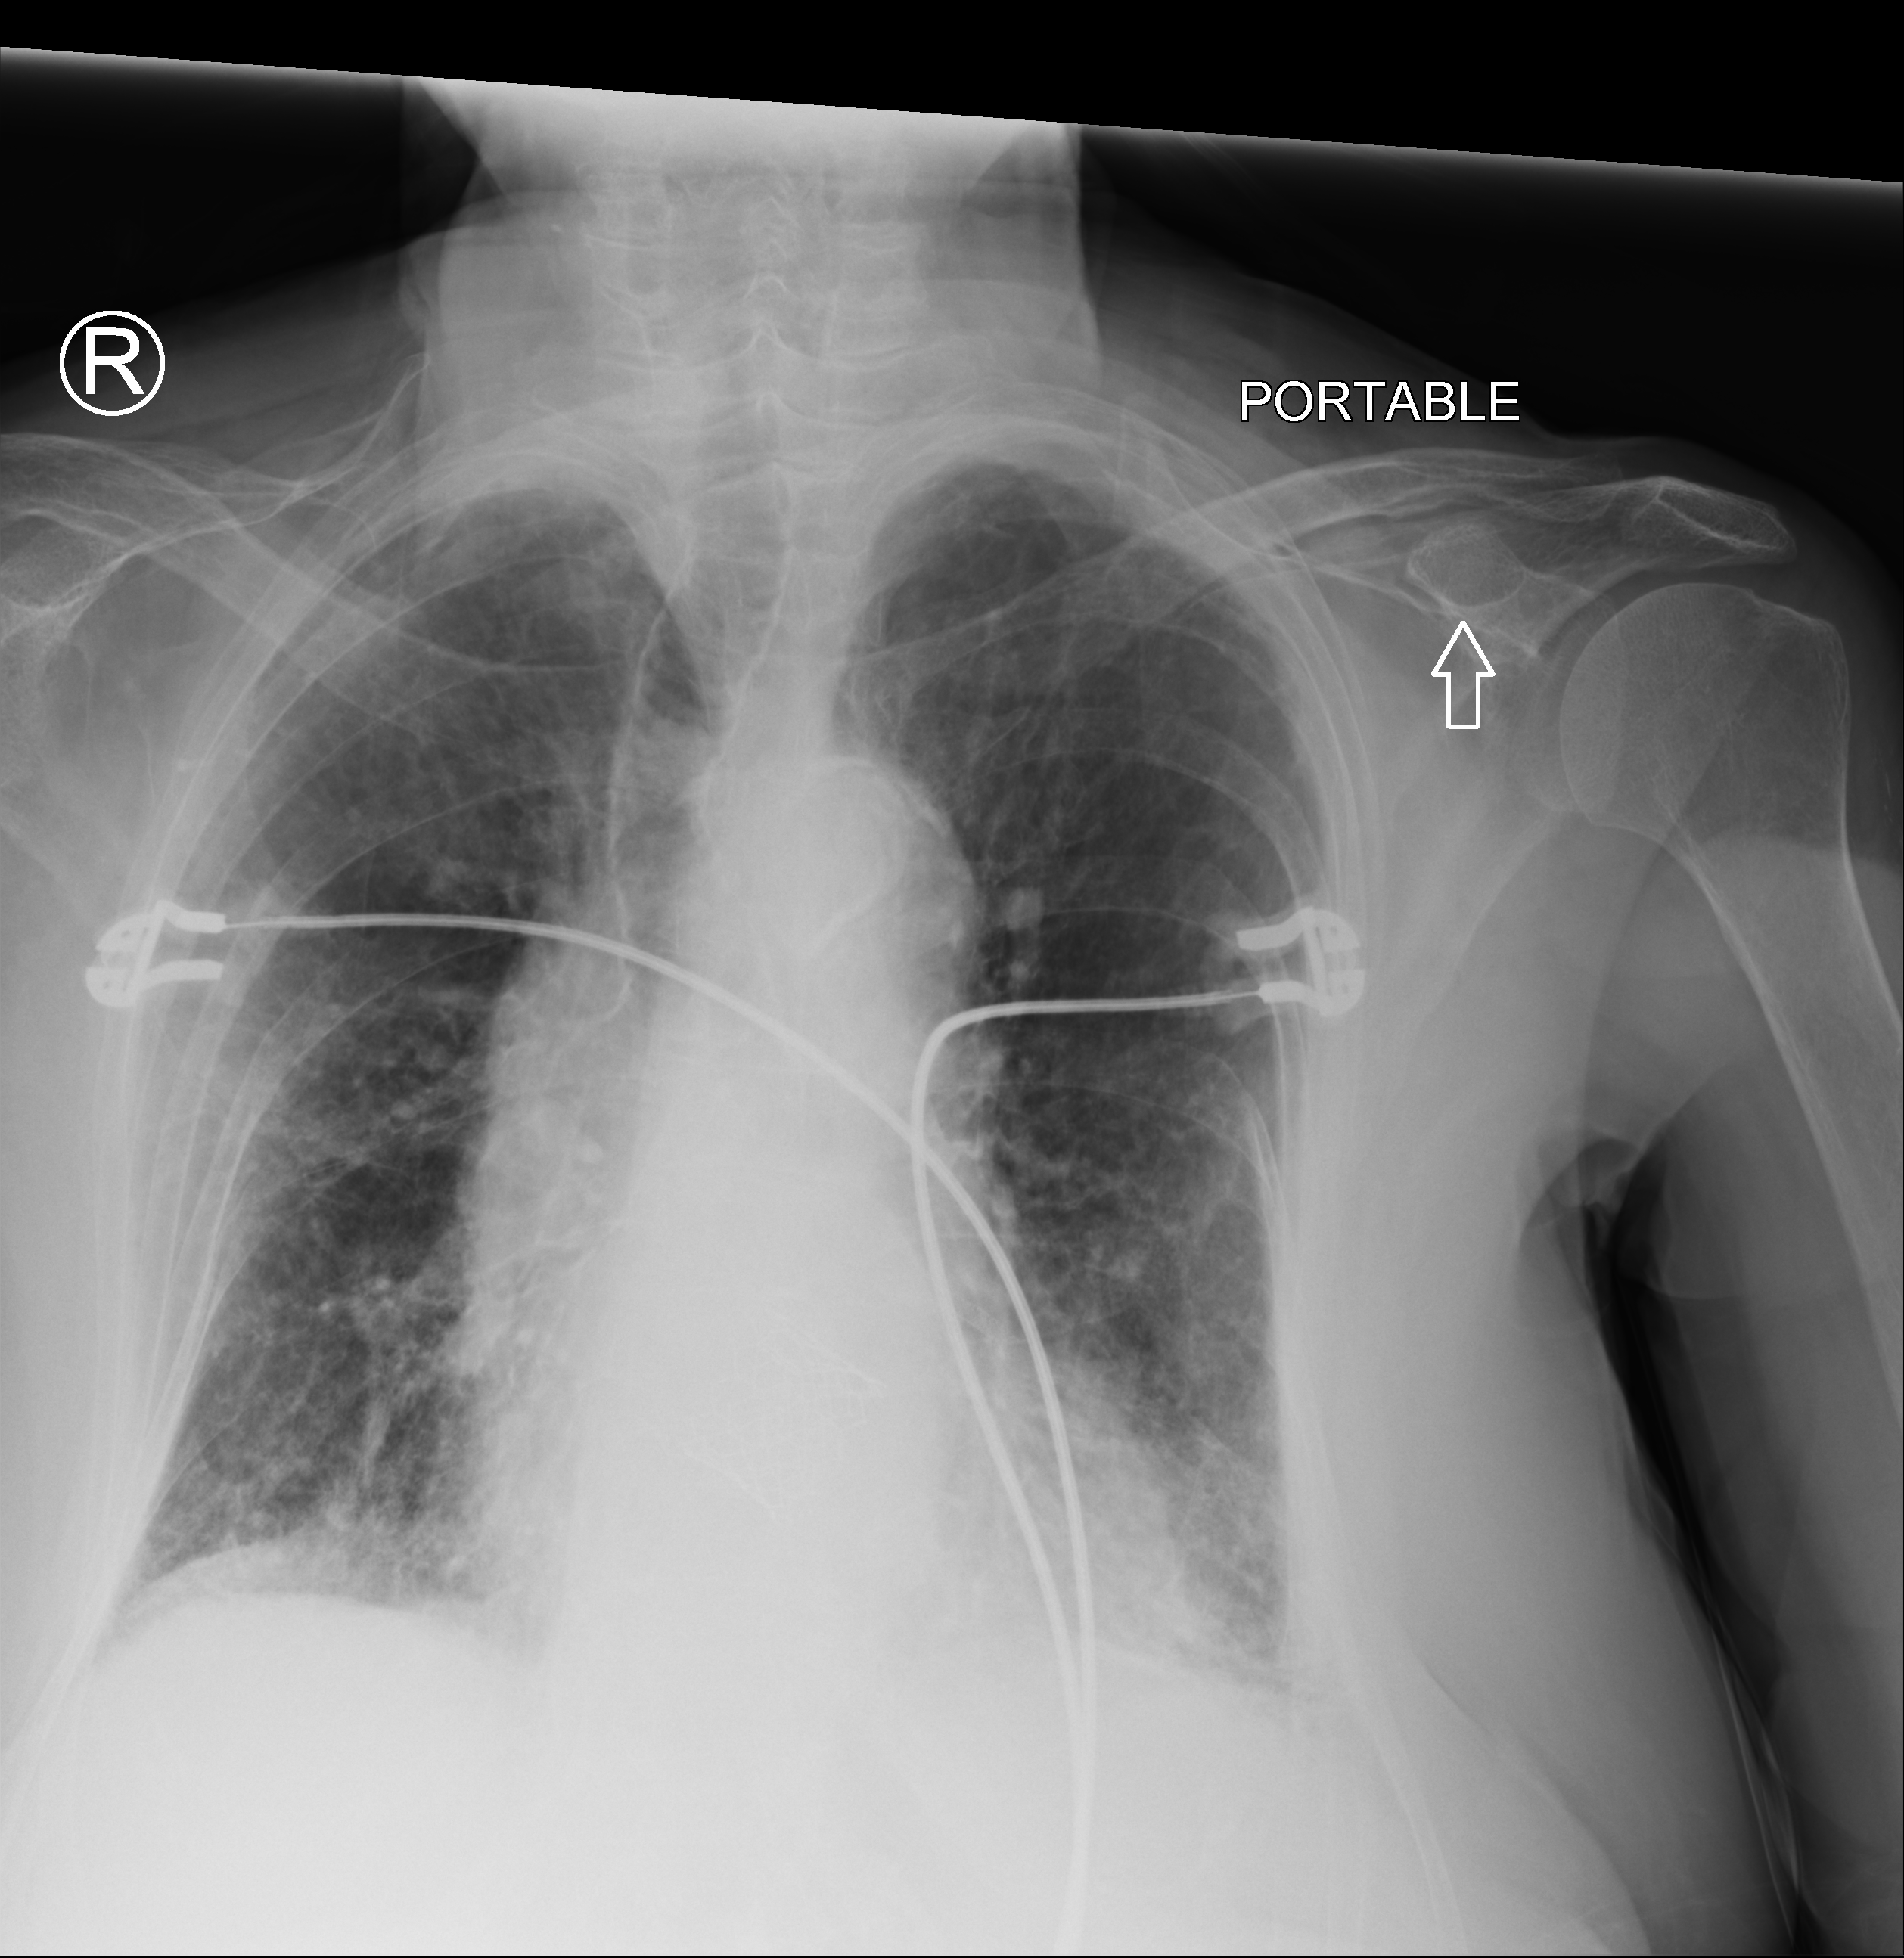
Bedside chest radiograph (computed radiography), anteroposterior (AP) projection. Female patient hospitalised with COVID-19, age 75–90 years.
From the hospital-stay record, not from the radiograph (when in the stay this image was taken is not recorded): smoking status (admission record): never; hypertension (admission record): no; length of hospital stay: 5 days.